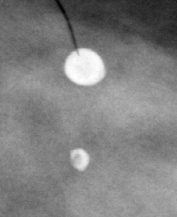
Region of interest cut from a scanned film mammogram (one marked finding), left breast, CC view.
- Marked abnormality: calcifications, morphology large rodlike / round and regular, distribution regional; BI-RADS assessment category 2; subtlety rating 5 on a 1 (subtle) to 5 (obvious) scale; benign without callback (not worked up further).